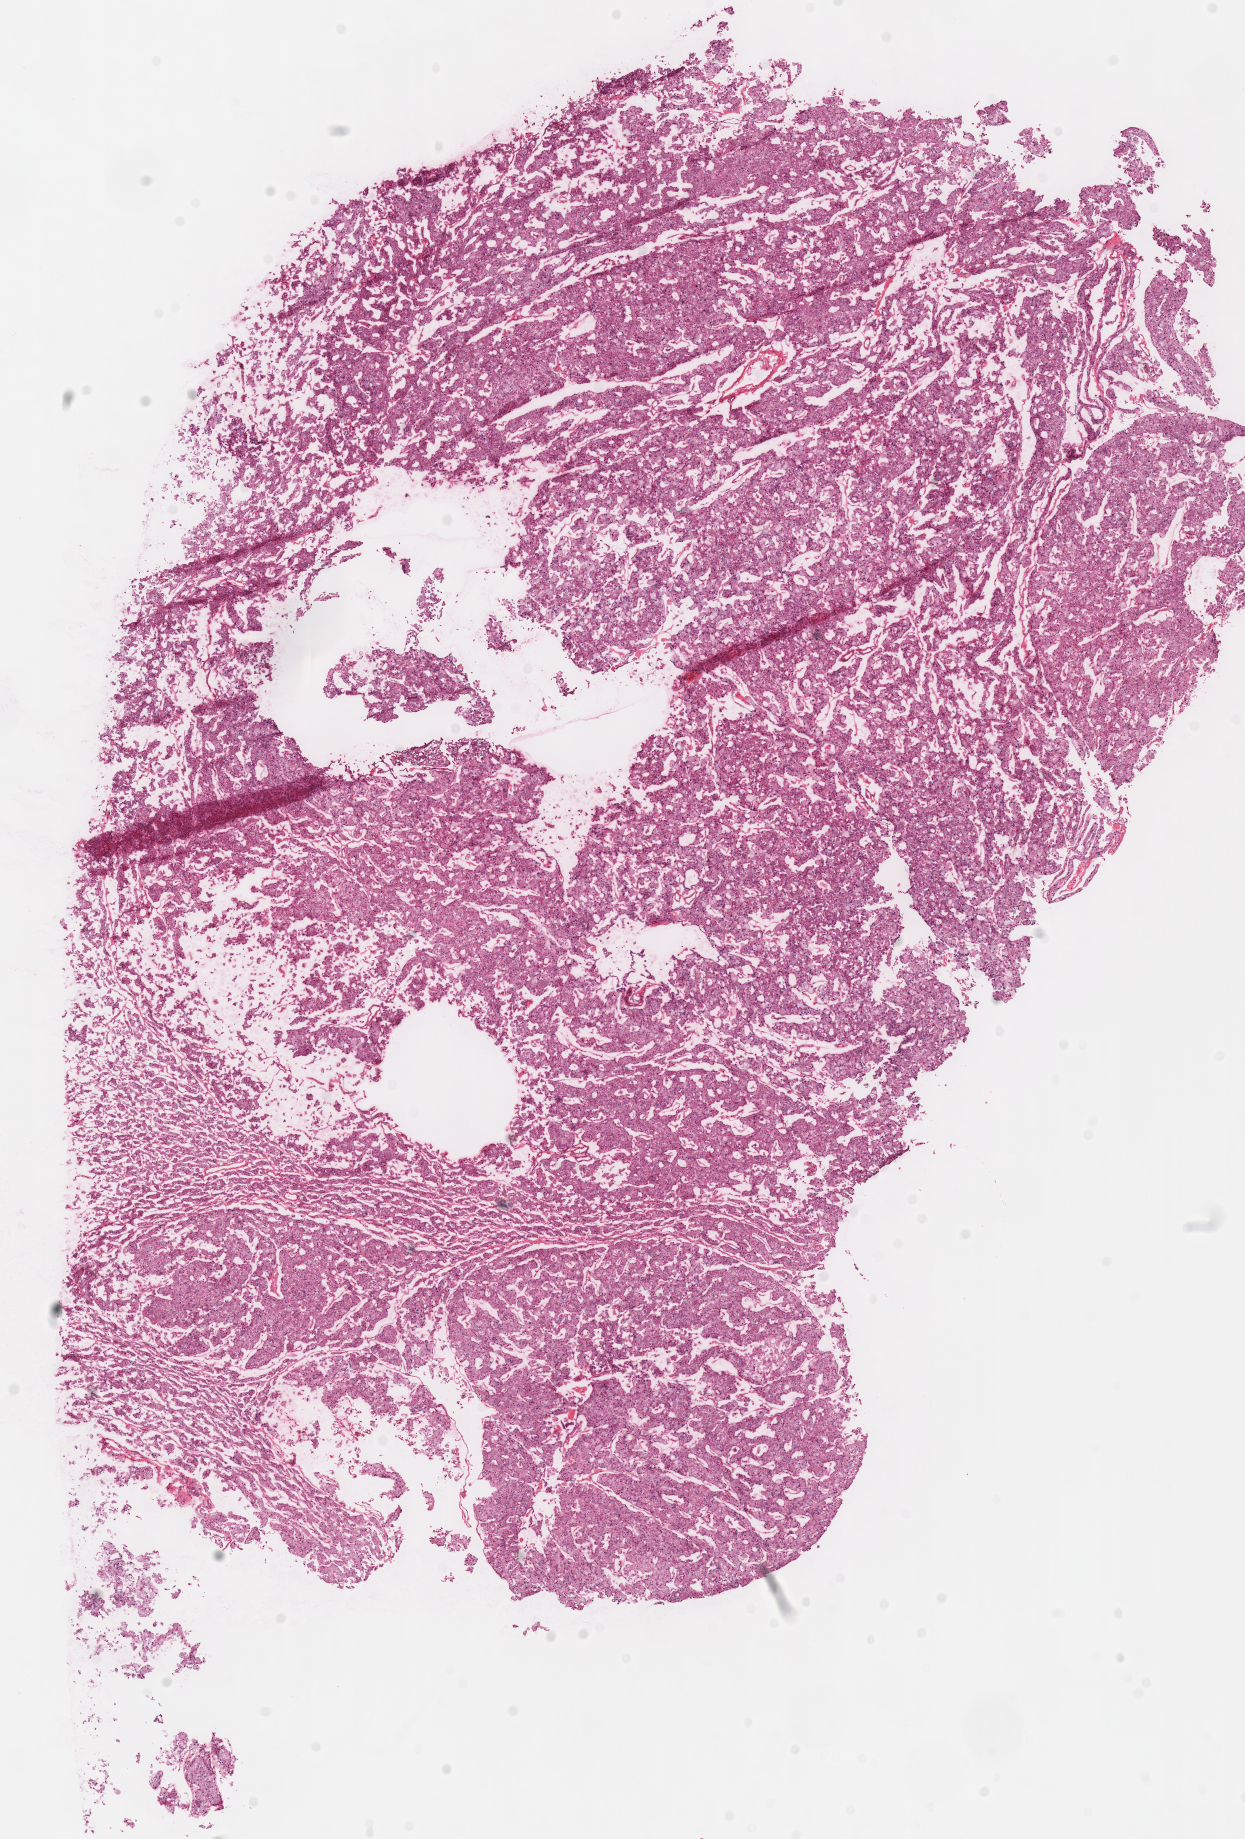
H&E whole-slide image — whole scanned area (about 9.8 x 14.5 mm, acquisition: 40x scan) shown as a low-resolution overview. Frozen section from the top of the tissue portion. Kidney, primary tumour sample. Female patient; age at initial diagnosis 67 years. Slide review estimates, as recorded: tumour cells 100%, tumour nuclei 90%, normal cells 0%, stromal cells 0%, necrosis 0%. Infiltration values recorded for this section: lymphocyte infiltration 1%, monocyte infiltration 0%, neutrophil infiltration 0%.
Diagnosis: Renal cell carcinoma, chromophobe type. AJCC pathologic stage: II. TNM: T2 NX M0.